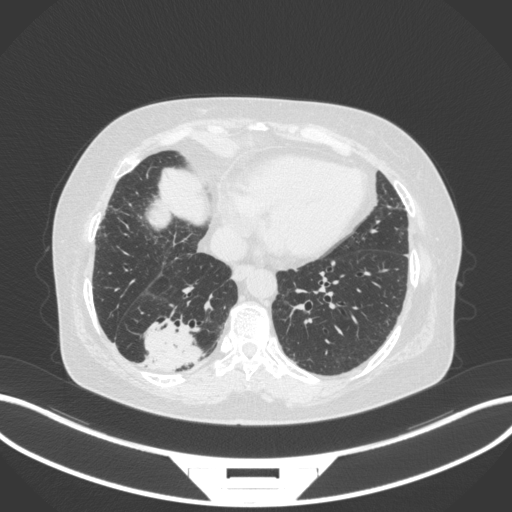
Chest CT, one axial slice. Position 66 of 303 along the scan axis. Lung window (W 1500 / L -600 HU). 1 mm slice thickness. 512 × 512 image matrix, field of view 400 × 400 mm. Patient: female, 65 years. Case-level facts recorded for this patient, not image findings: clinical TNM (as recorded): T2b N1 M0; histopathological grade: G1.
Outlined on this slice (rectangle marked by the reading radiologist):
- lung tumour (recorded histology: adenocarcinoma): box from (x=132, y=316) to (x=206, y=372) px